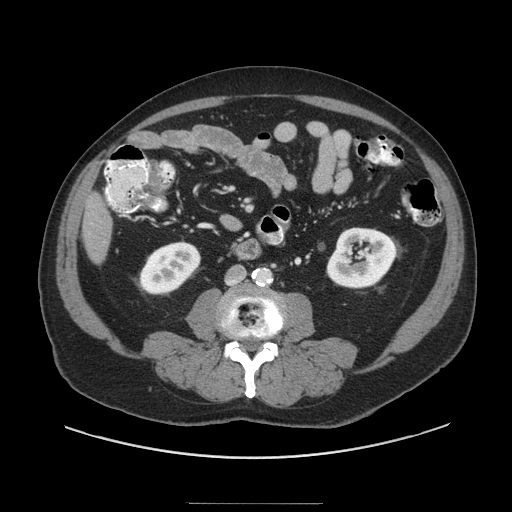
Contrast-enhanced abdominal CT (liver protocol), one axial slice; slice 17 of 91 in the series (ordered by position); reconstruction kernel STANDARD; soft-tissue window (W 400 / L 40 HU); 2.5 mm slice thickness; 512 × 512 image matrix, field of view 440 × 440 mm. Case-level facts recorded for this patient, not image findings: diagnosis: hepatocellular carcinoma (patient treated with transarterial chemoembolisation; whether this scan precedes or follows treatment is not stated here); TNM stage (as recorded): Stage-I; Child-Pugh class: A; tumour differentiation: well differentiated; tumour size: 4 cm.
Structures marked on this image (semi-automatic segmentation, software-assisted and operator-edited):
- liver parenchyma outside the tumour (the mass and vessels are separate outlines, so this box may not span the whole liver): bounding box <82,194,112,262> (left, top, right, bottom; pixels)